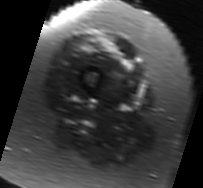
MRI of an extremity soft-tissue mass, one axial slice; position 13 of 91 along the scan axis; T2-weighted fat-saturated; MR volume resampled by the dataset authors to the PET/CT grid (not the native acquisition matrix); 3.27 mm slice thickness; 203 × 188 image matrix, field of view 198 × 184 mm. Female patient. From the clinical record (not read from this slice): histological type: malignant solitary fibrous tumor; grade: intermediate; site of the primary tumour: right thigh.
Structures marked on this image (expert contour drawn on MRI and transferred to this co-registered scan by the dataset authors):
- gross tumour volume including surrounding oedema: box from (x=83, y=35) to (x=134, y=68) px